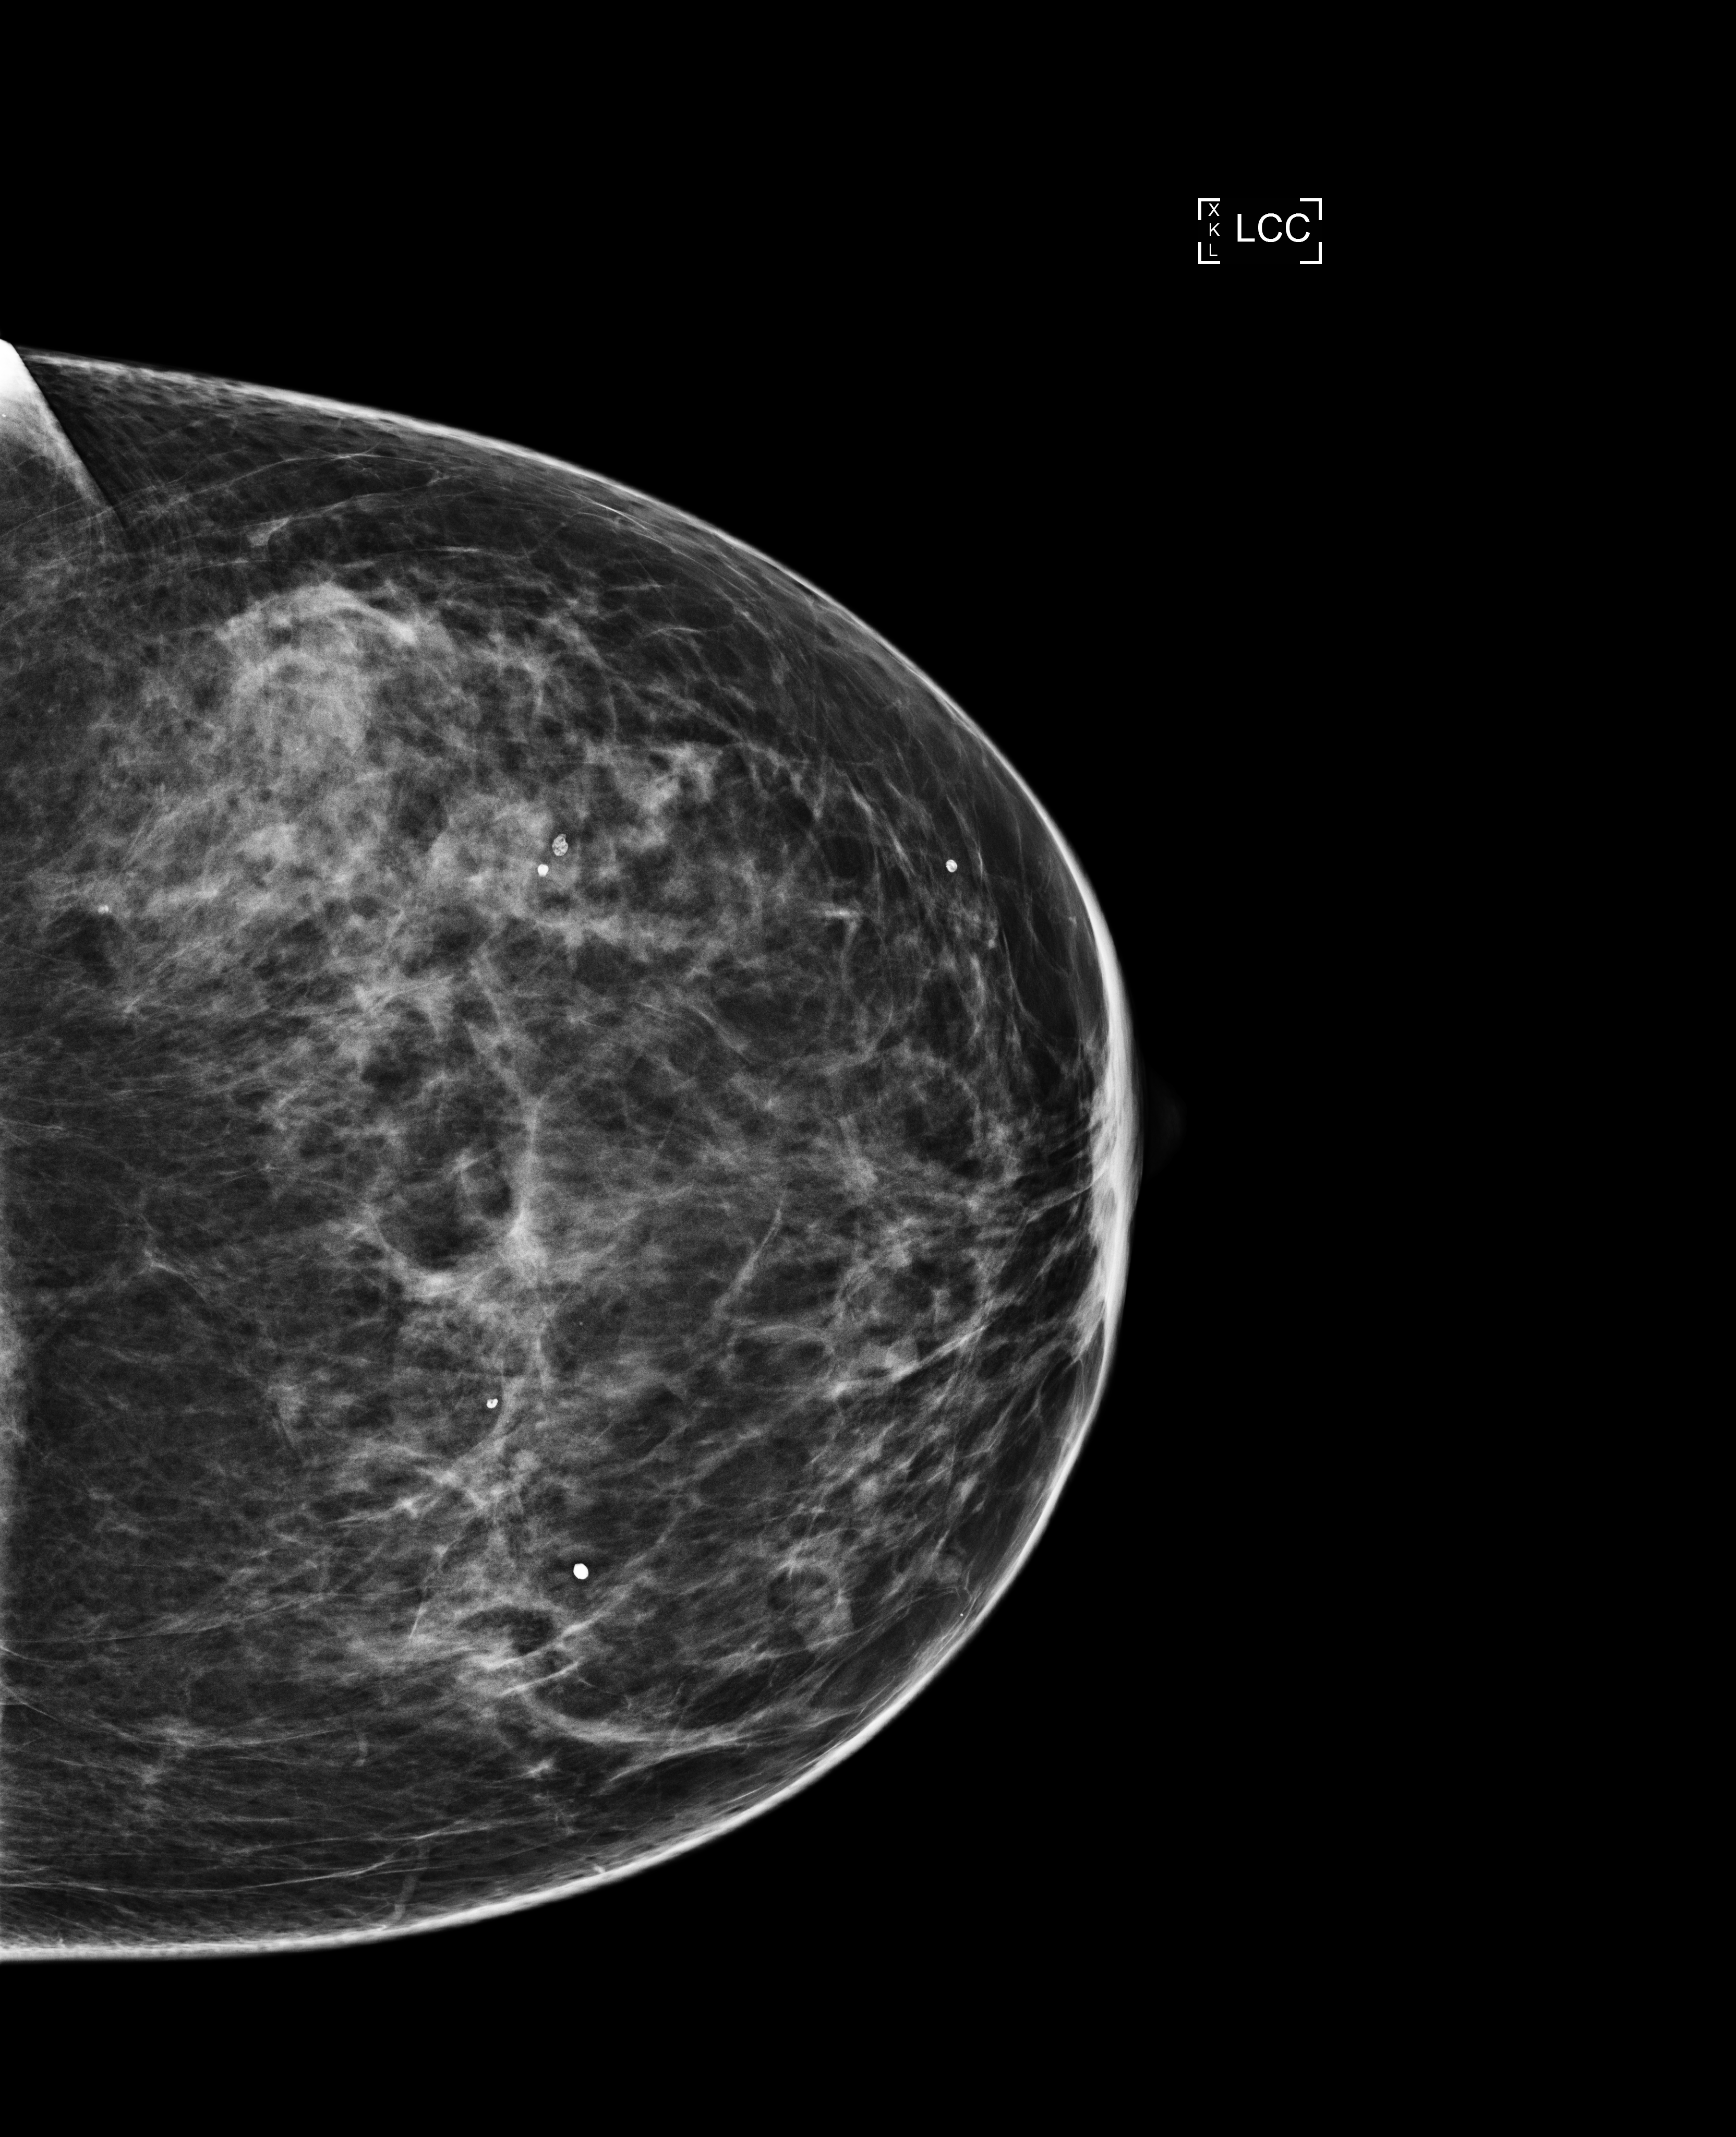
Annual screening mammography examination. Female patient, age 46 years.
Image type: full-field digital mammogram. Breast: left. Projection: craniocaudal (CC) view.